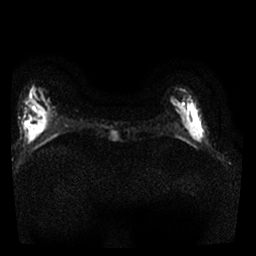
Breast MRI, one axial slice; slice 6 of 25 in the series (ordered by position); diffusion-weighted series; image 2 of 4 stored at this slice position (different b-values; order by instance number); 1.5 T; 4 mm slice thickness; 256 × 256 image matrix, field of view 300 × 300 mm. Female patient.
Structures marked on this image (manually delineated by an expert):
- tumour on diffusion-weighted imaging: bounding box [x1, y1, x2, y2] px = [169, 96, 203, 143]